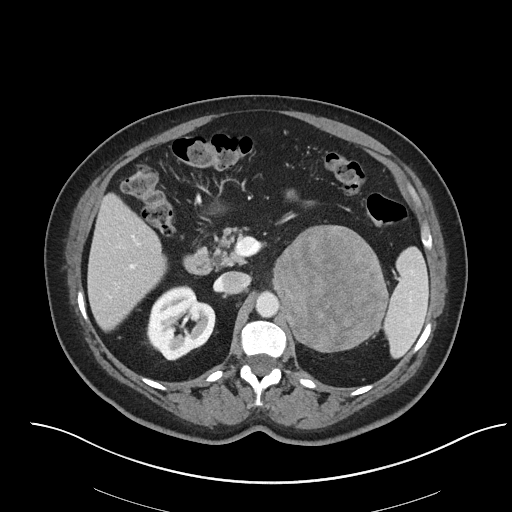
Contrast-enhanced abdominal CT, one axial slice; position 45 of 92 along the scan axis; reconstruction kernel I40f/2; 120 kVp; intravenous contrast given; soft-tissue window (W 400 / L 40 HU); 512 × 512 image matrix, field of view 440 × 440 mm. Patient: female, 53 years. From the clinical record (not read from this slice): diagnosis: adrenocortical carcinoma; tumour side: left adrenal.
Outlined on this slice (semi-automatic segmentation, software-assisted and operator-edited):
- mass: bounding box [x1, y1, x2, y2] px = [275, 226, 387, 351]